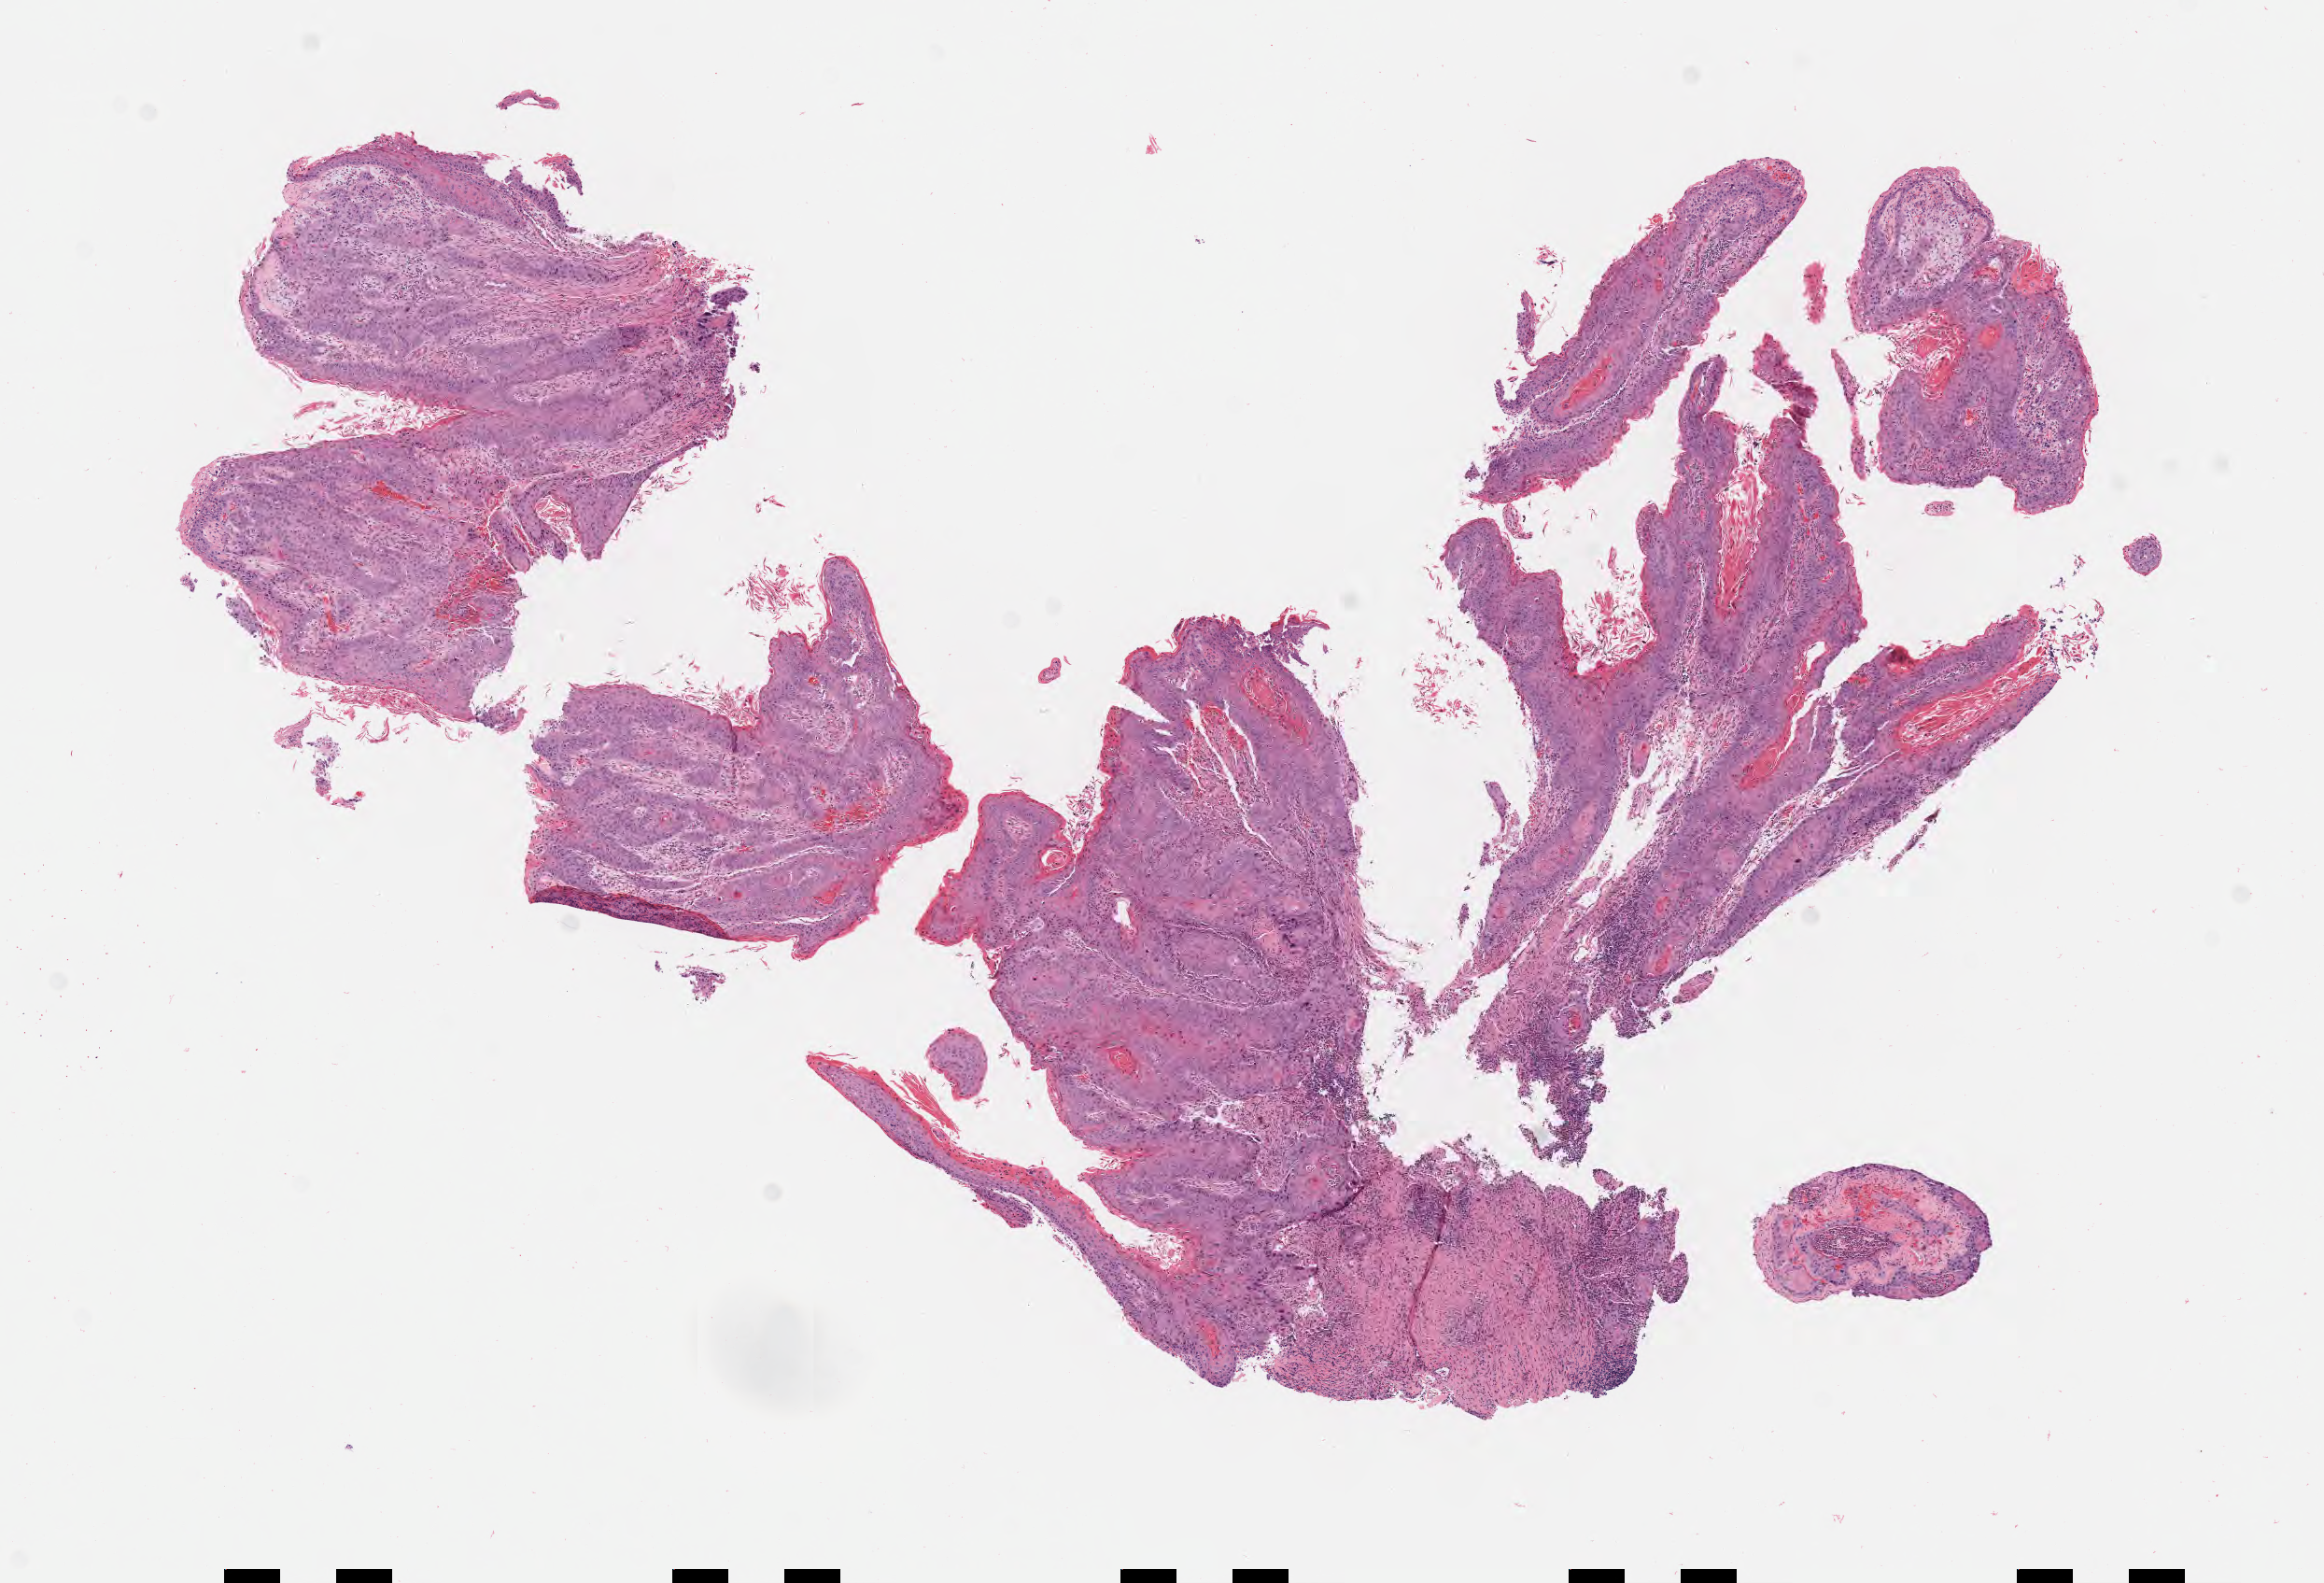
Whole-slide image, H&E stain — low-resolution overview of the scanned area, about 10.1 x 6.9 mm; specimen: tumor tissue; anatomic site: cervix. Female patient, aged 68.
Histologic diagnosis: Squamous cell carcinoma, keratinizing, NOS.